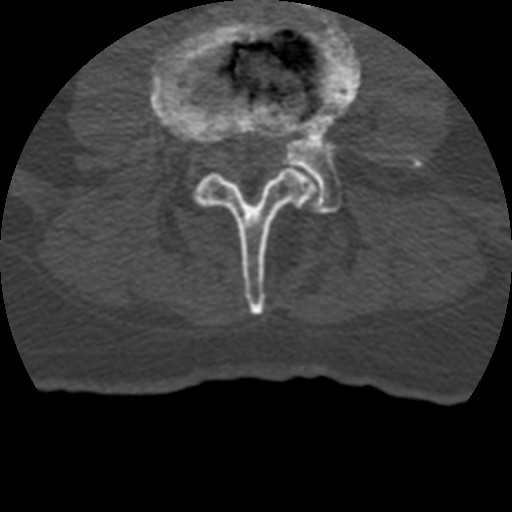
CT including the spine, one axial slice. Slice 79 of 399 in the series (ordered by position). 120 kVp. Bone window (W 1800 / L 400 HU). 1.25 mm slice thickness. 512 × 512 image matrix, field of view 160 × 160 mm. Patient age 69 years. Case-level facts recorded for this patient, not image findings: primary cancer: prostate.
Annotated regions visible in this slice (semi-automatic segmentation, software-assisted and operator-edited):
- L3 vertebra: bounding box <149,18,317,315> (left, top, right, bottom; pixels)
- L4 vertebra: <284,10,422,213>